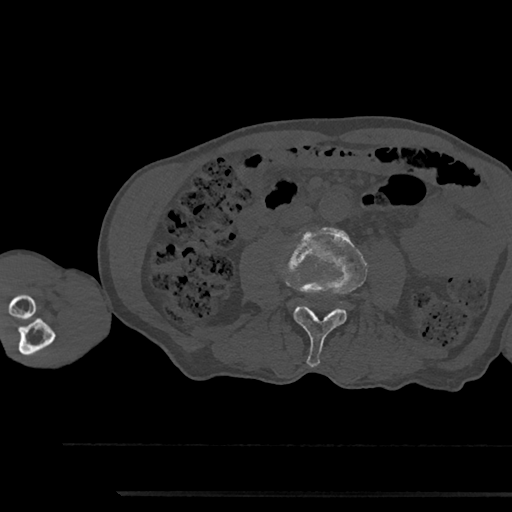
CT including the spine, one axial slice. Slice 467 of 797 in the series (ordered by position). Reconstruction kernel Br40s/3. 120 kVp. Bone window (W 1800 / L 400 HU). 0.5 mm slice thickness. 512 × 512 image matrix, field of view 367 × 367 mm. Male patient, age 79 years. Case-level facts recorded for this patient, not image findings: primary cancer: prostate.
Annotated regions visible in this slice (semi-automatic segmentation, software-assisted and operator-edited):
- L3 vertebra: bounding box <281,228,367,367> (left, top, right, bottom; pixels)